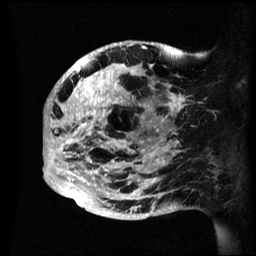
Breast MRI (dynamic contrast-enhanced), one sagittal slice; slice 21 of 60 in the series (ordered by position); dynamic contrast-enhanced series, image 2 of 3 at this slice position (ordered by acquisition); 1.5 T; TE 4.2 ms, TR 8.4 ms; 2.4 mm slice thickness; 256 × 256 image matrix, field of view 230 × 230 mm. Patient: female, 48 years.
Annotated regions visible in this slice (semi-automatic segmentation, software-assisted and operator-edited):
- analysis volume of interest (the breast-tissue region the enhancement analysis was run in; not a lesion): bounding box (x1, y1, x2, y2) in pixels: (44, 41, 195, 220)
- tumour enhancement mask (voxels above the 70 % enhancement threshold inside the analysis volume of interest): (44, 42, 183, 207)